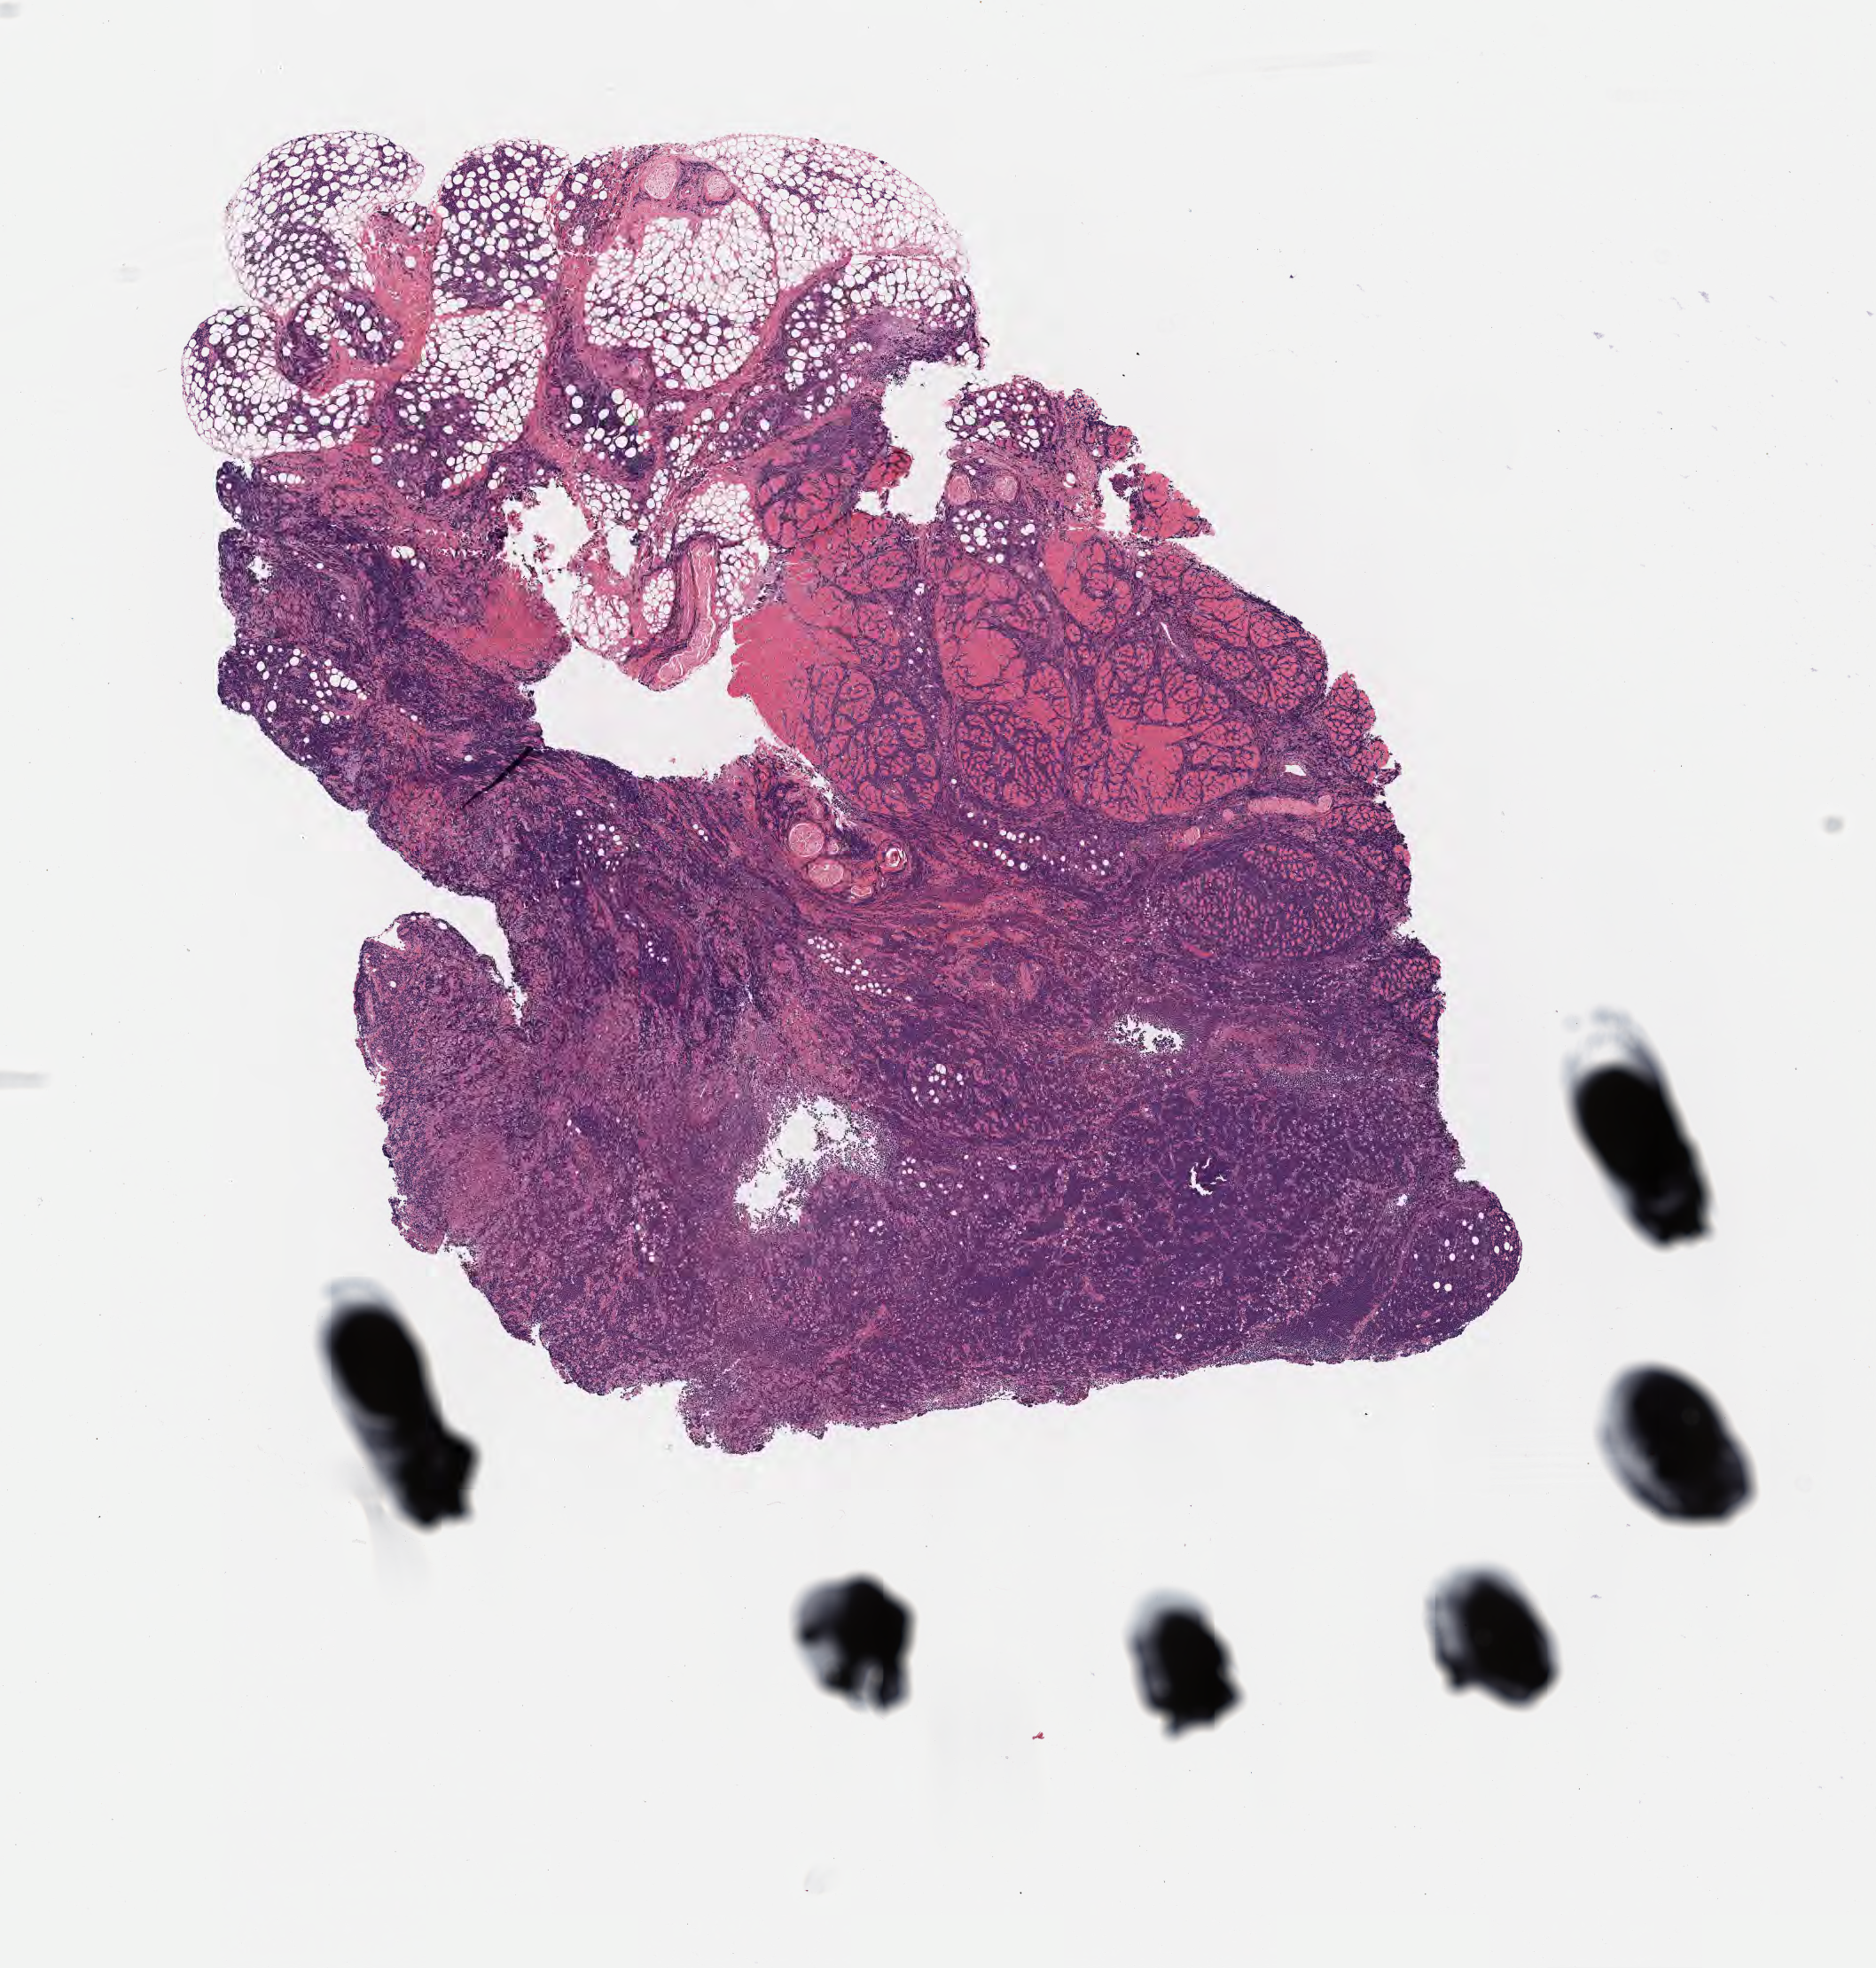
Digitized haematoxylin and eosin-stained section, whole scanned area (about 8.6 x 9.0 mm) shown as a low-resolution overview. Specimen: tumor tissue. Anatomic site: mouth. Male patient; age at initial diagnosis 9 years.
Diagnosis: Burkitt lymphoma, NOS.